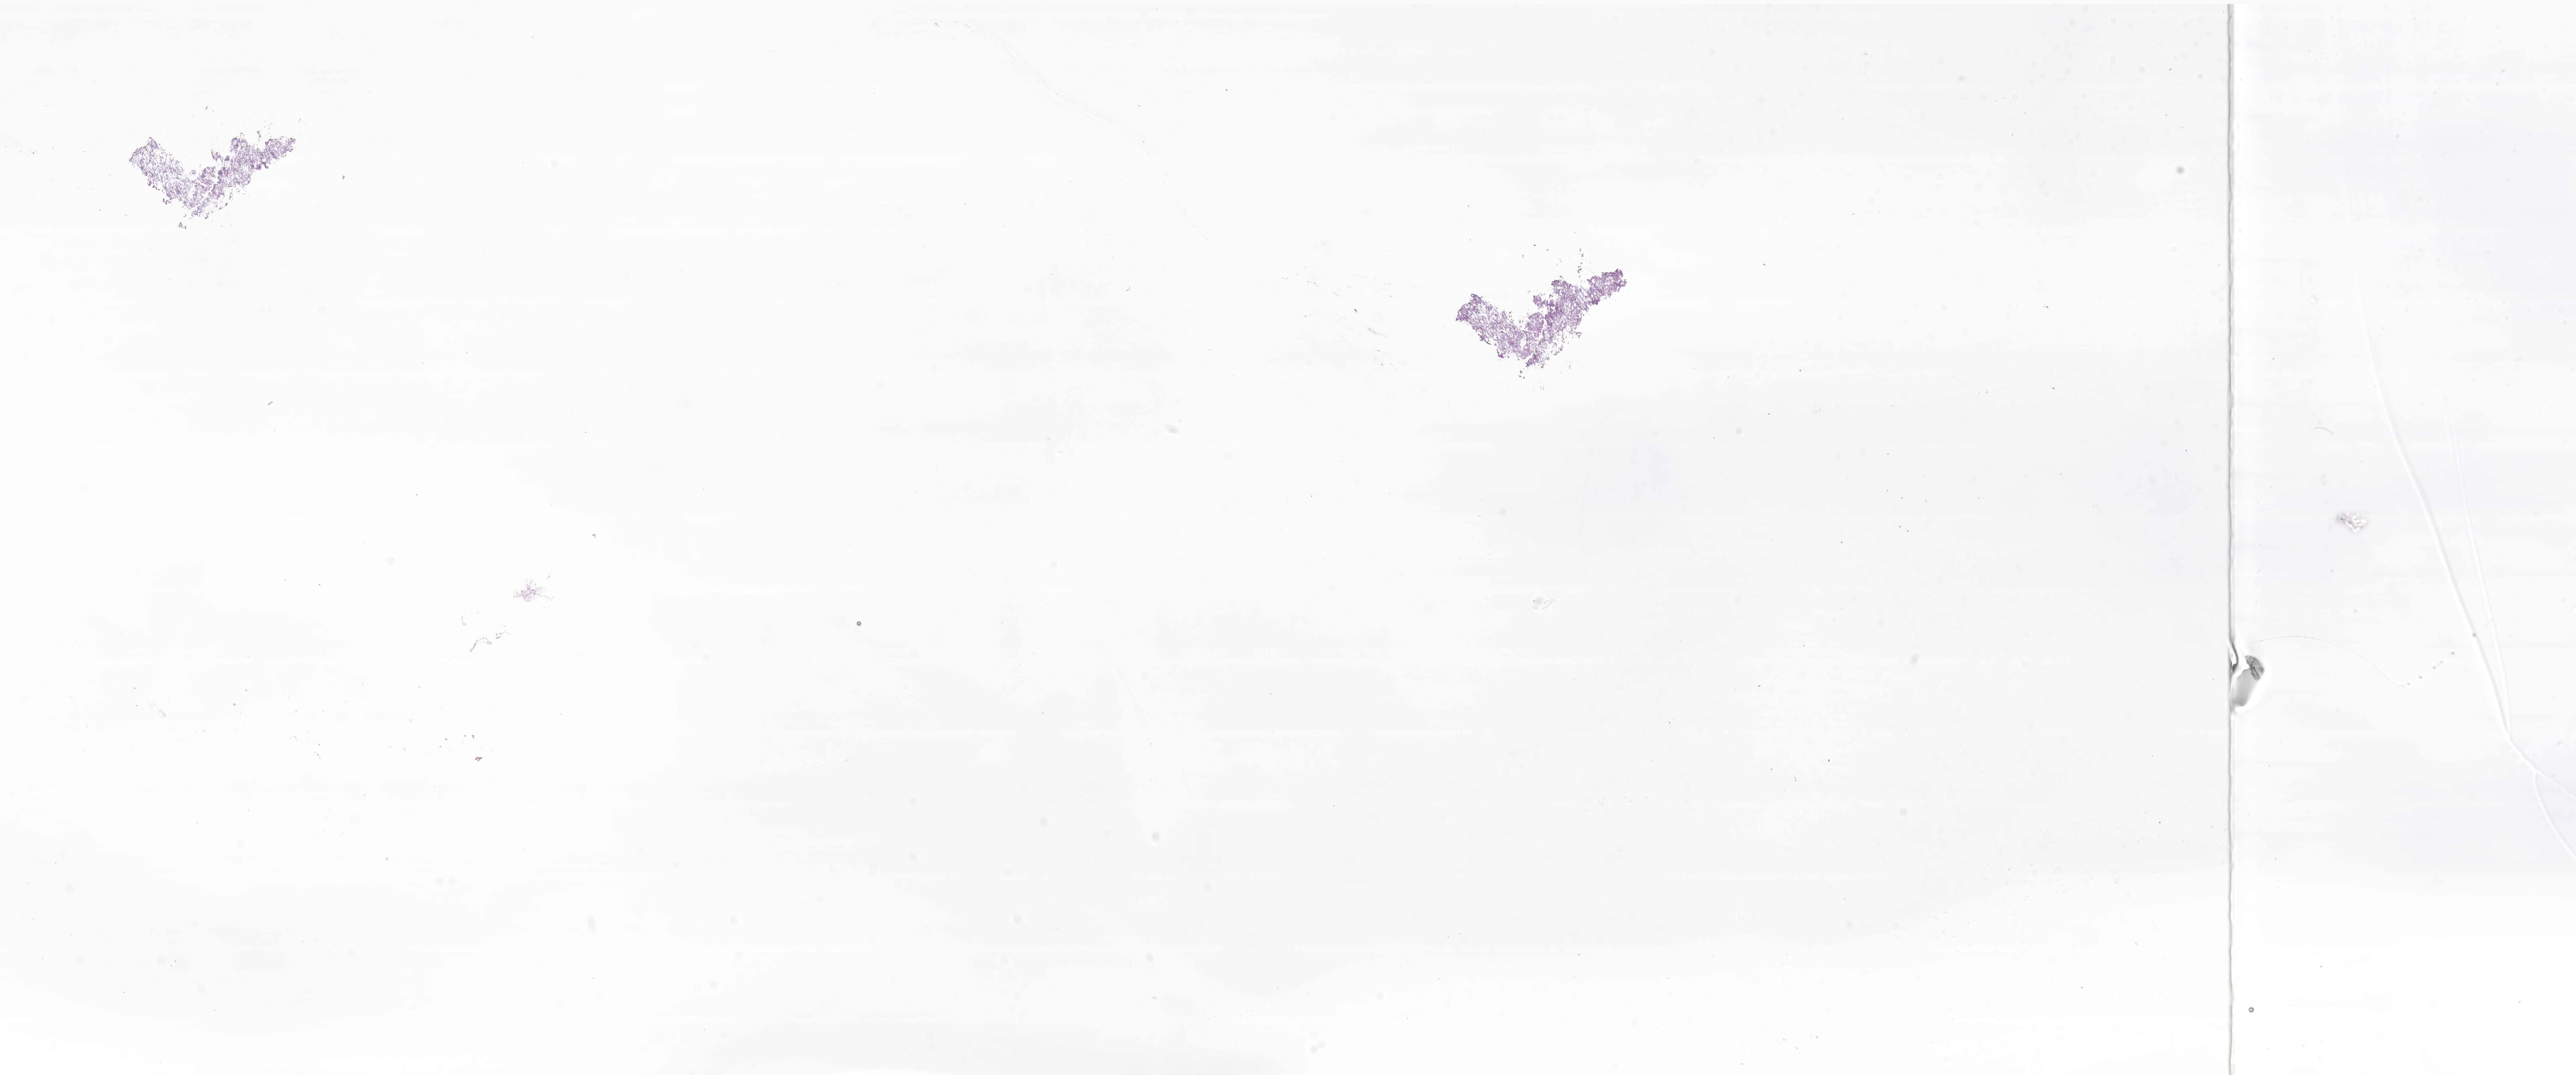
Digitized H&E-stained section of tumor tissue from the brain — low-resolution overview of the scanned area, about 38.3 x 16.0 mm; cryosection (OCT / tissue freezing medium). Patient female; age 61 months (5 years 1 month).
Recorded diagnosis: Pilocytic astrocytoma.